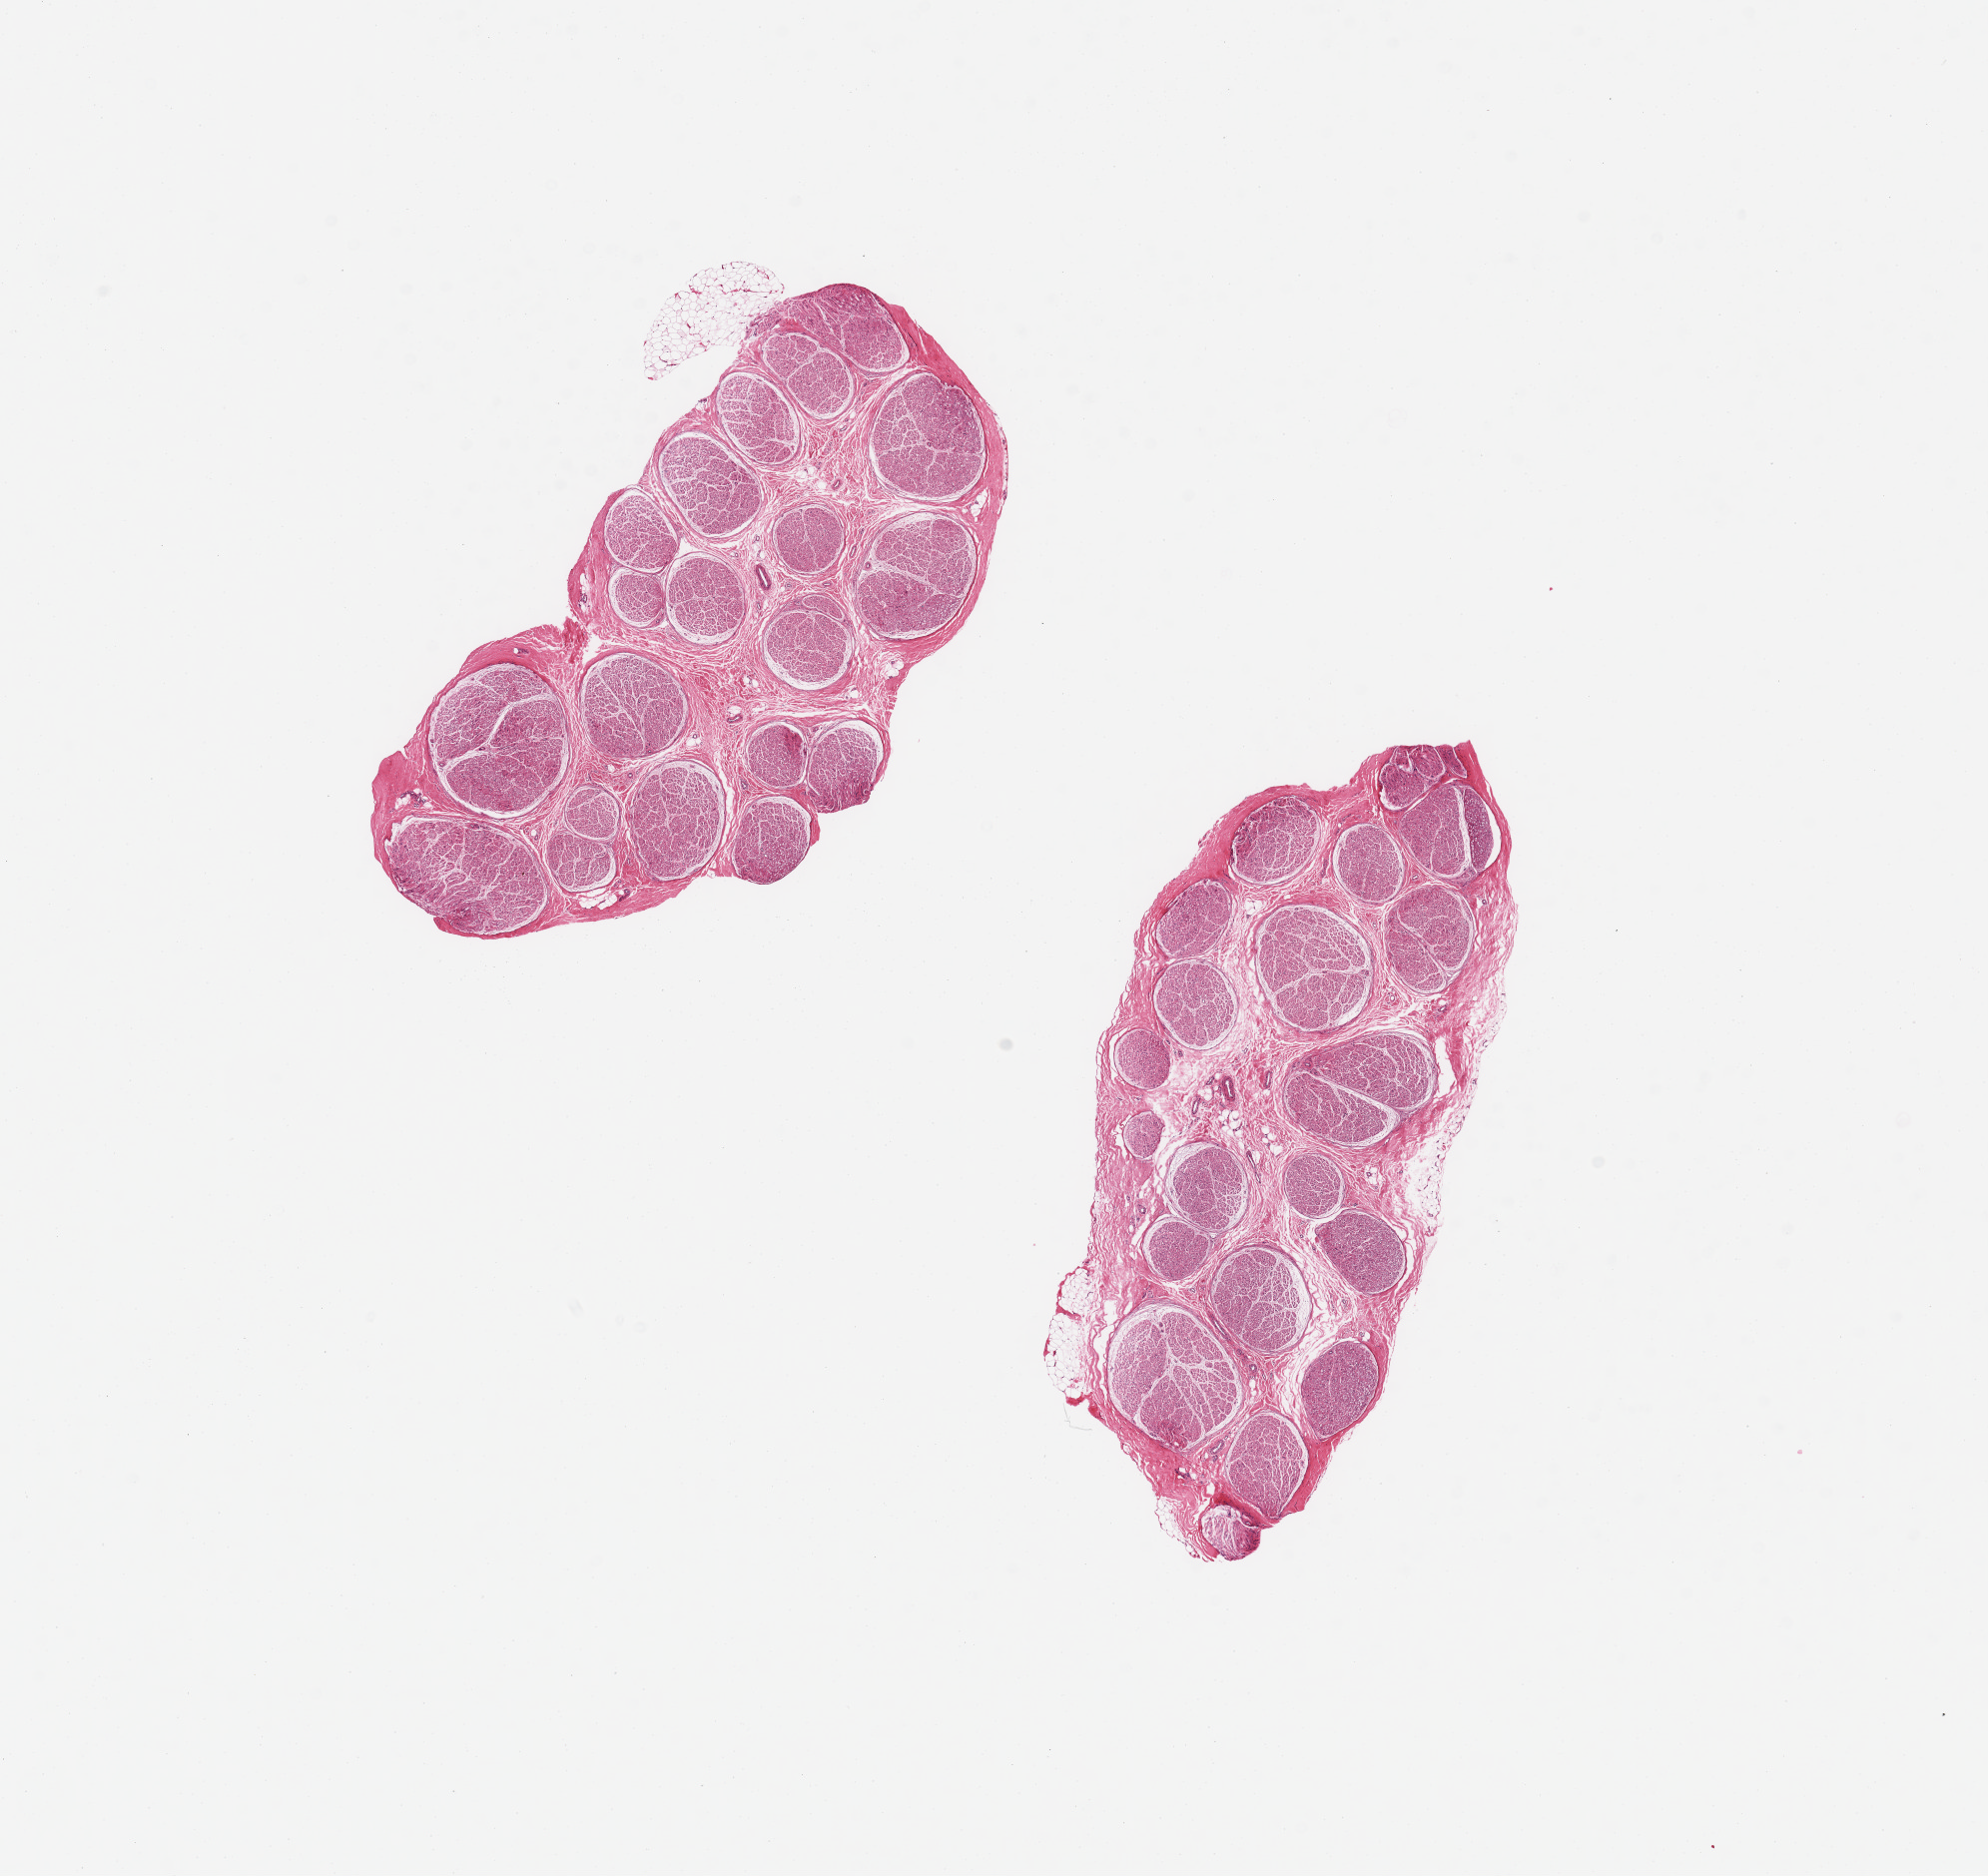
Whole-slide image, H&E stain, brightfield — low-resolution overview of the scanned area, about 15.8 x 14.9 mm (acquisition: 20x scan), PAXgene-fixed, paraffin-embedded tissue, sampled site (target tissue): tibial nerve, donor tissue sample.
Review note (as recorded): 2 pieces: well trimmed.